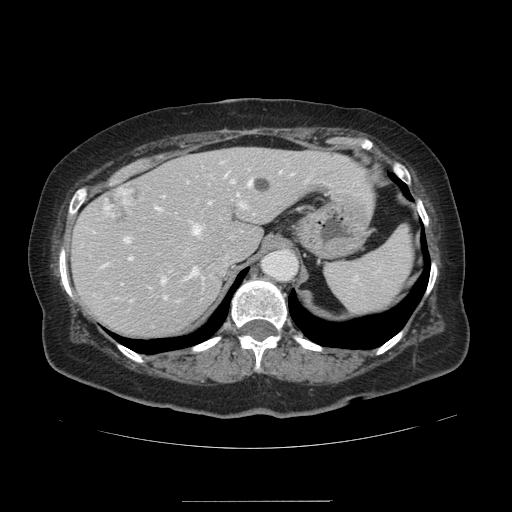
Contrast-enhanced abdominal CT, one axial slice; slice 95 of 141 in the series (ordered by position); 120 kVp; soft-tissue window (W 400 / L 40 HU); 2.5 mm slice thickness; 512 × 512 image matrix, field of view 393 × 393 mm. Female patient, age 74 years. From the clinical record (not read from this slice): diagnosis: colorectal cancer liver metastases, imaged before liver resection; multiple liver metastases: yes; largest metastasis: 7 cm.
Annotated regions visible in this slice (manually delineated by an expert):
- hepatic veins: box from (x=154, y=171) to (x=281, y=281) px
- liver: (x=73, y=148)–(x=371, y=339)
- planned liver remnant (the part of the liver to remain after resection): (x=74, y=148)–(x=371, y=339)
- portal vein (with intrahepatic branches): (x=124, y=173)–(x=292, y=301)
- liver metastasis: (x=251, y=178)–(x=272, y=193)
- liver metastasis: (x=91, y=186)–(x=136, y=227)